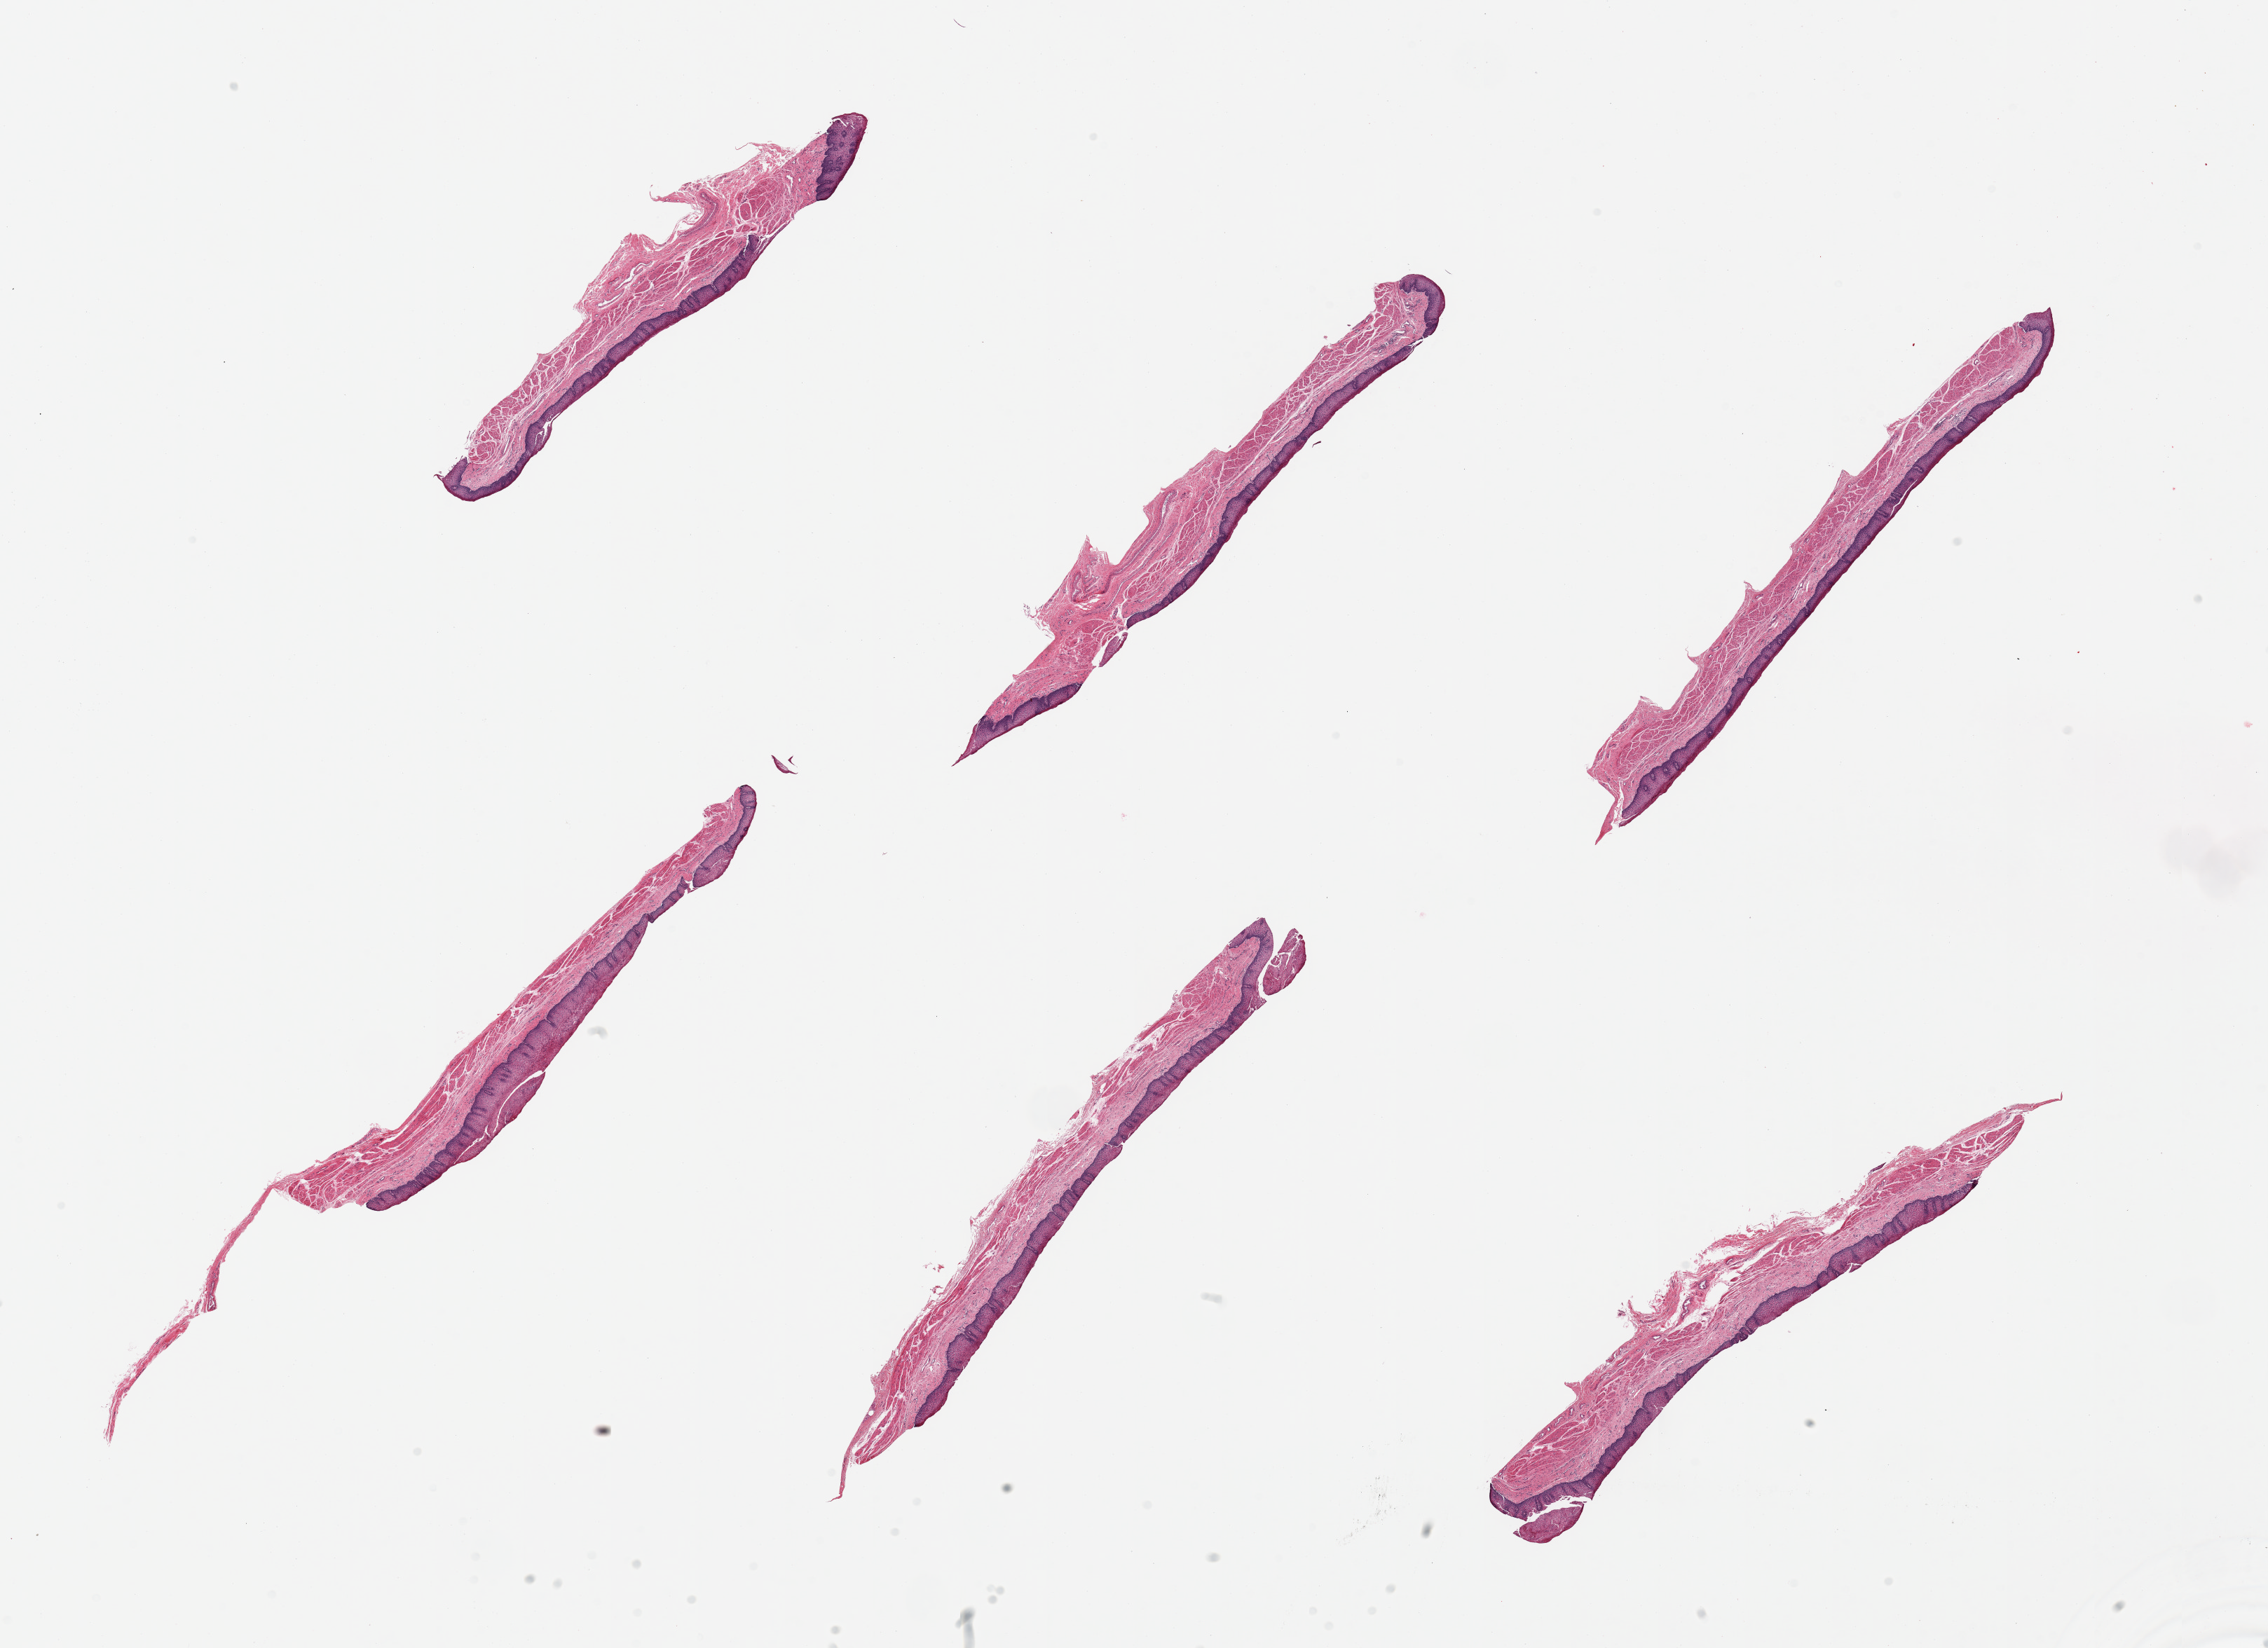
H&E whole-slide image, a low-resolution overview of the entire scanned area, about 25.6 x 18.6 mm (slide scanned at 20x); PAXgene-fixed paraffin-embedded (PFPE) section; target tissue: esophageal mucous membrane; donor tissue sample.
Reviewer comment on this tissue sample: 6 pieces.